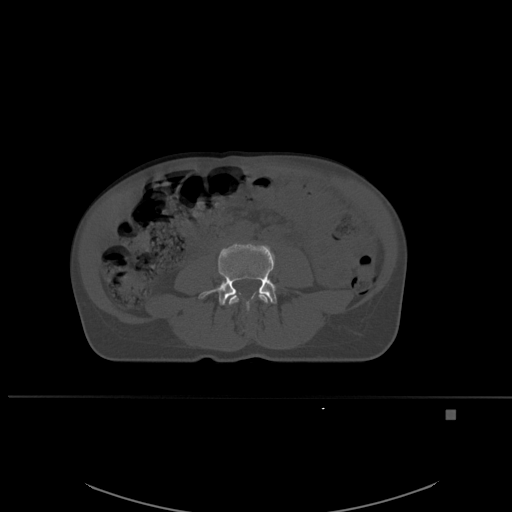
CT including the spine, one axial slice. Bone window (W 1800 / L 400 HU). 1.5 mm slice thickness. 512 × 512 image matrix, field of view 440 × 440 mm. Female patient, age 45 years. From the clinical record (not read from this slice): primary cancer: lung.
Outlined on this slice (semi-automatic segmentation, software-assisted and operator-edited):
- L3 vertebra: bounding box [x1, y1, x2, y2] px = [228, 293, 269, 305]
- L4 vertebra: [198, 243, 277, 310]